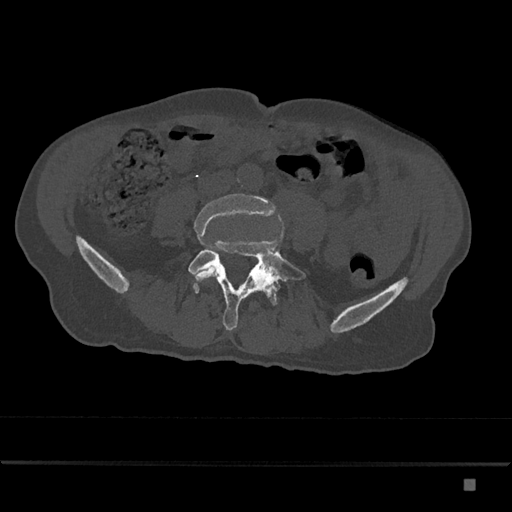
CT including the spine, one axial slice. Reconstruction kernel Br40s/3. 120 kVp. Bone window (W 1800 / L 400 HU). 0.5 mm slice thickness. 512 × 512 image matrix, field of view 390 × 390 mm. Male patient, age 72 years. Case-level facts recorded for this patient, not image findings: primary cancer: prostate.
Outlined on this slice (semi-automatic segmentation, software-assisted and operator-edited):
- L4 vertebra: bounding box (x1, y1, x2, y2) in pixels: (193, 193, 276, 281)
- L5 vertebra: (188, 239, 306, 331)